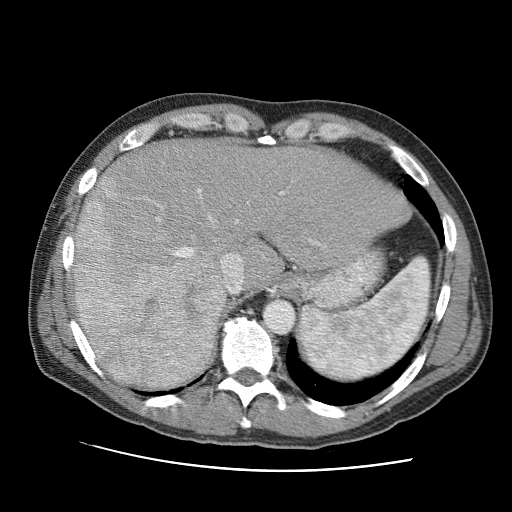
Contrast-enhanced abdominal CT (liver protocol), one axial slice. Position 73 of 95 along the scan axis. 120 kVp. One of 2 acquisitions stored at this slice position. Soft-tissue window (W 400 / L 40 HU). 2.5 mm slice thickness. 512 × 512 image matrix. Case-level facts recorded for this patient, not image findings: diagnosis: hepatocellular carcinoma (patient treated with transarterial chemoembolisation; whether this scan precedes or follows treatment is not stated here); TNM stage (as recorded): Stage-IVA; Child-Pugh class: A; tumour differentiation: moderately differentiated; tumour nodularity: multinodular.
Annotated regions visible in this slice (semi-automatic segmentation, software-assisted and operator-edited):
- liver parenchyma outside the tumour (the mass and vessels are separate outlines, so this box may not span the whole liver): box from (x=74, y=140) to (x=410, y=363) px
- mass: (x=75, y=173)–(x=227, y=392)
- liver vessels: (x=101, y=189)–(x=321, y=322)